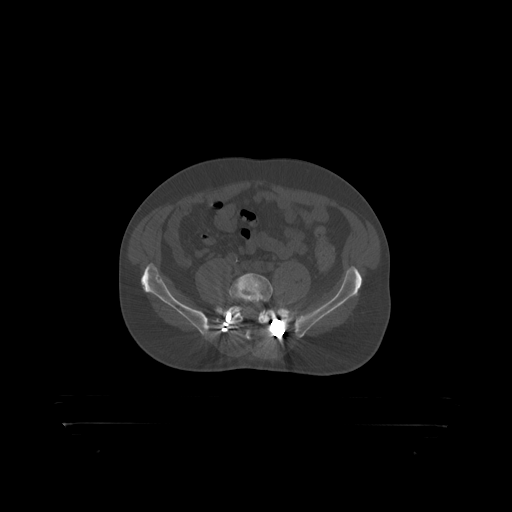
CT including the spine, one axial slice; position 197 of 399 along the scan axis; reconstruction kernel STANDARD; 120 kVp; bone window (W 1800 / L 400 HU); 1.25 mm slice thickness; 512 × 512 image matrix, field of view 650 × 650 mm. Male patient, age 46 years. From the clinical record (not read from this slice): primary cancer: skin.
Outlined on this slice (semi-automatically segmented with operator editing):
- L5 vertebra: bounding box <230,273,273,319> (left, top, right, bottom; pixels)